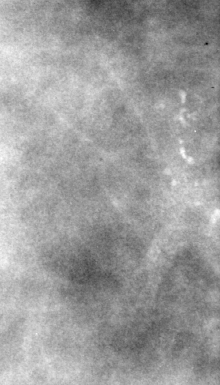
Cropped region of a digitized screen-film mammogram centred on a radiologist-marked abnormality; right breast; CC view; BI-RADS breast density category 4 (scale 1–4).
Calcifications, morphology pleomorphic, distribution clustered; BI-RADS assessment category 4; pathology (as recorded): malignant.